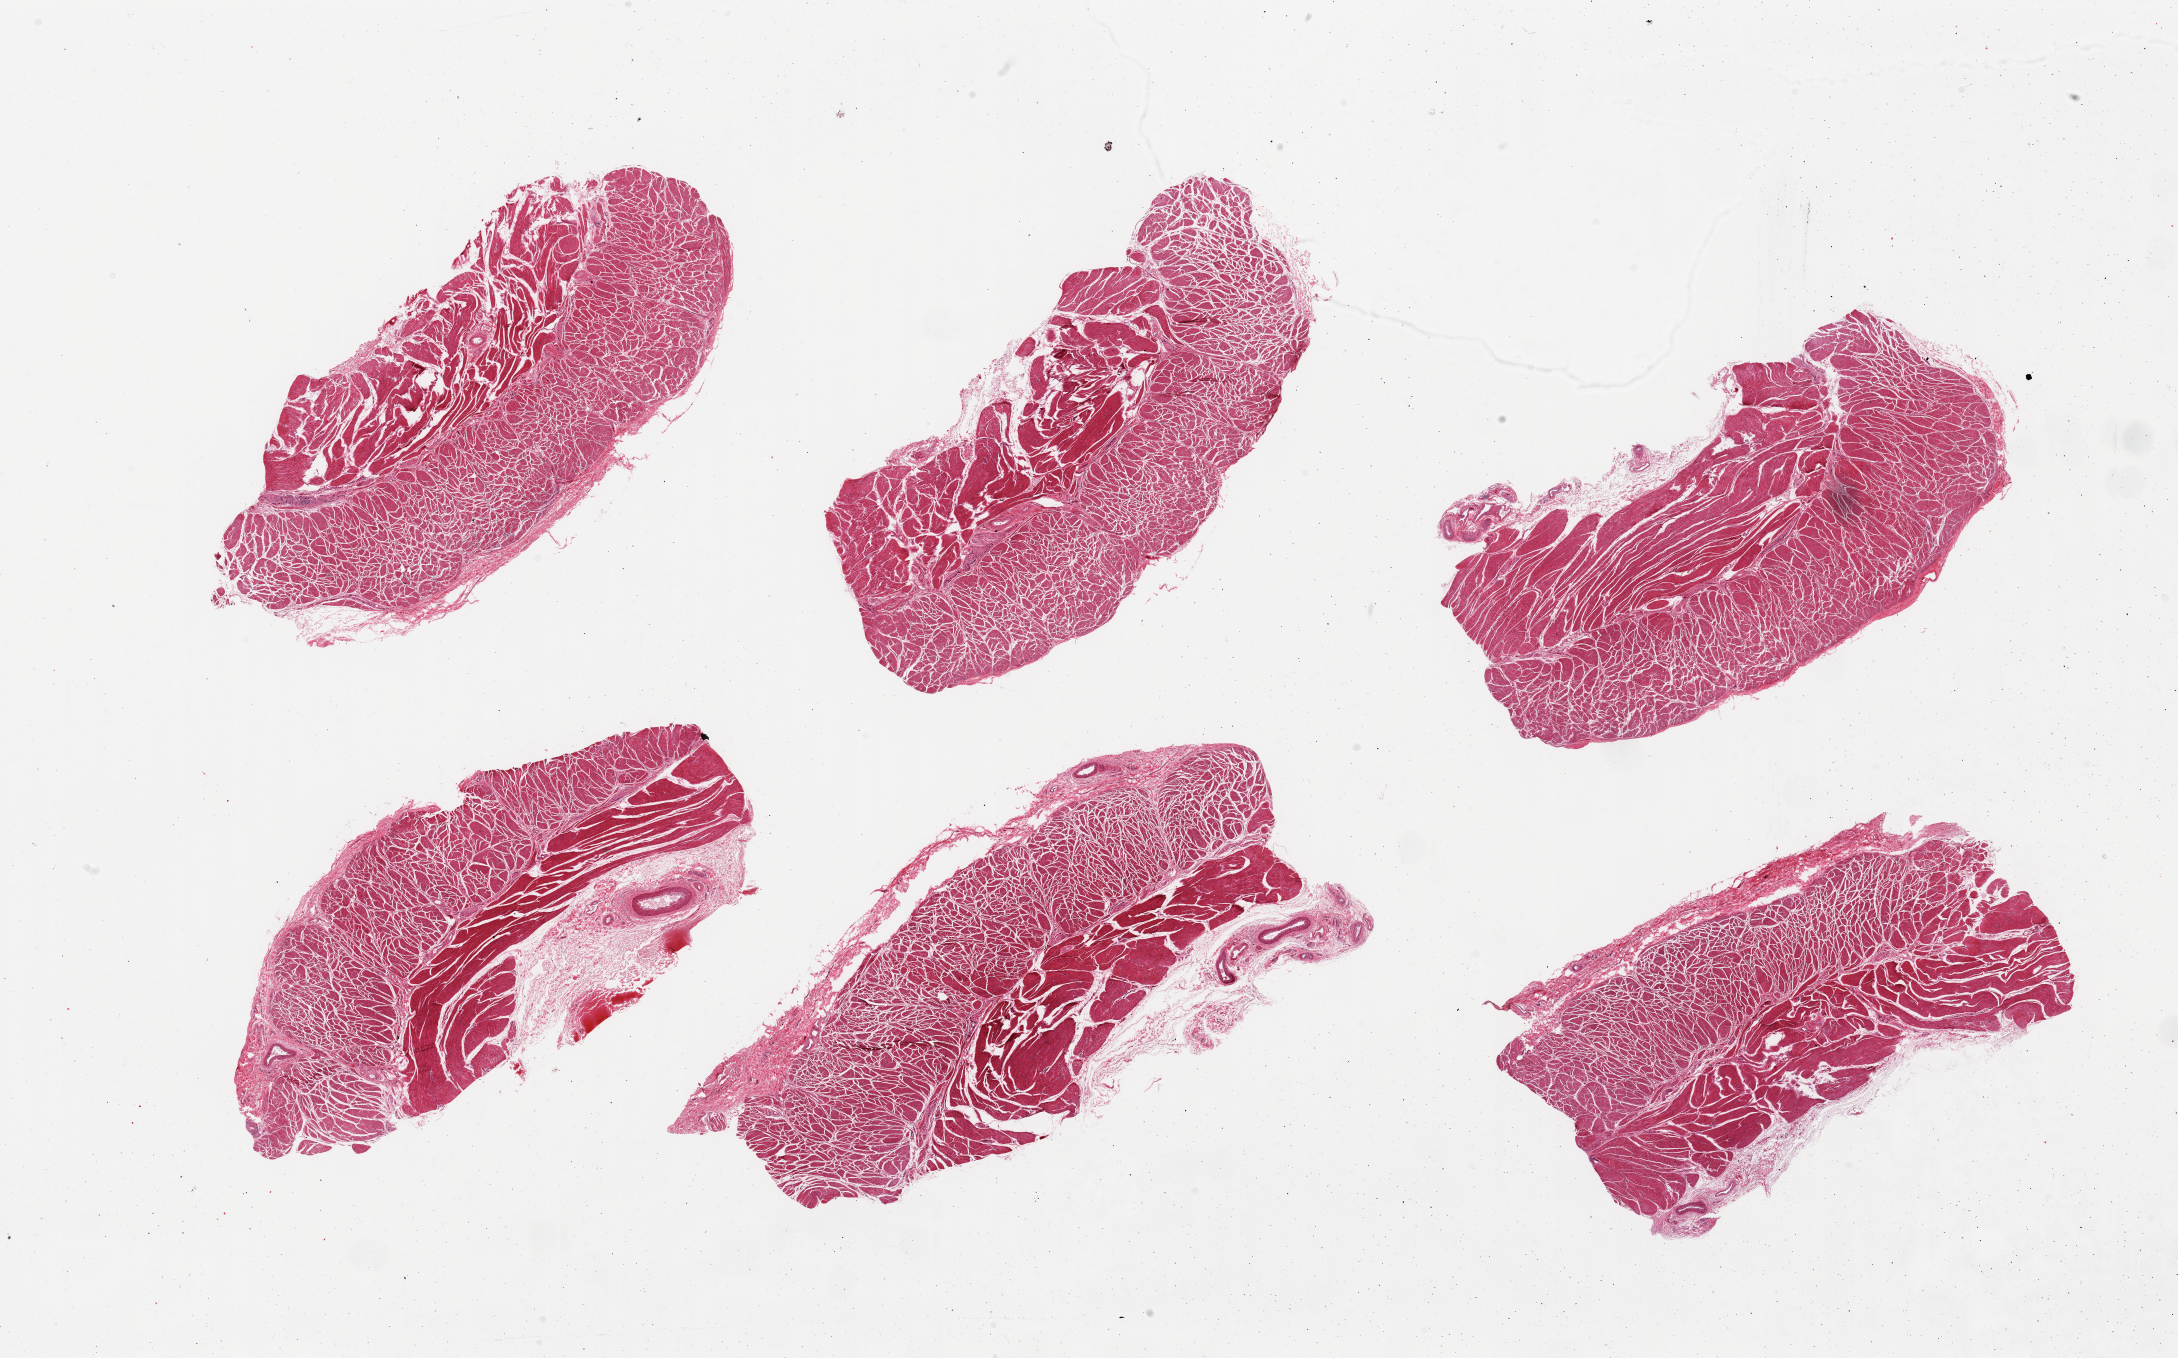
H&E whole-slide image — shown as a low-resolution overview of the whole scanned area (about 34.5 x 21.5 mm). PAXgene-fixed, paraffin-embedded tissue. Section of esophageal muscle (target tissue). Donor tissue sample. Donor: female.
- reviewer comment on this tissue sample: 6 pieces, all muscularis, good specimens